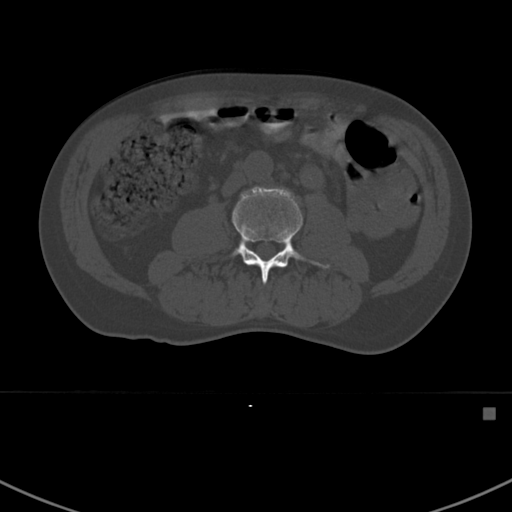
CT including the spine, one axial slice. Slice 263 of 412 in the series (ordered by position). Reconstruction kernel Br40s. 120 kVp. Bone window (W 1800 / L 400 HU). 512 × 512 image matrix. Male patient, age 59 years. From the clinical record (not read from this slice): primary cancer: prostate.
Annotated regions visible in this slice (semi-automatic segmentation, software-assisted and operator-edited):
- L3 vertebra: bounding box (x1, y1, x2, y2) in pixels: (230, 186, 330, 284)